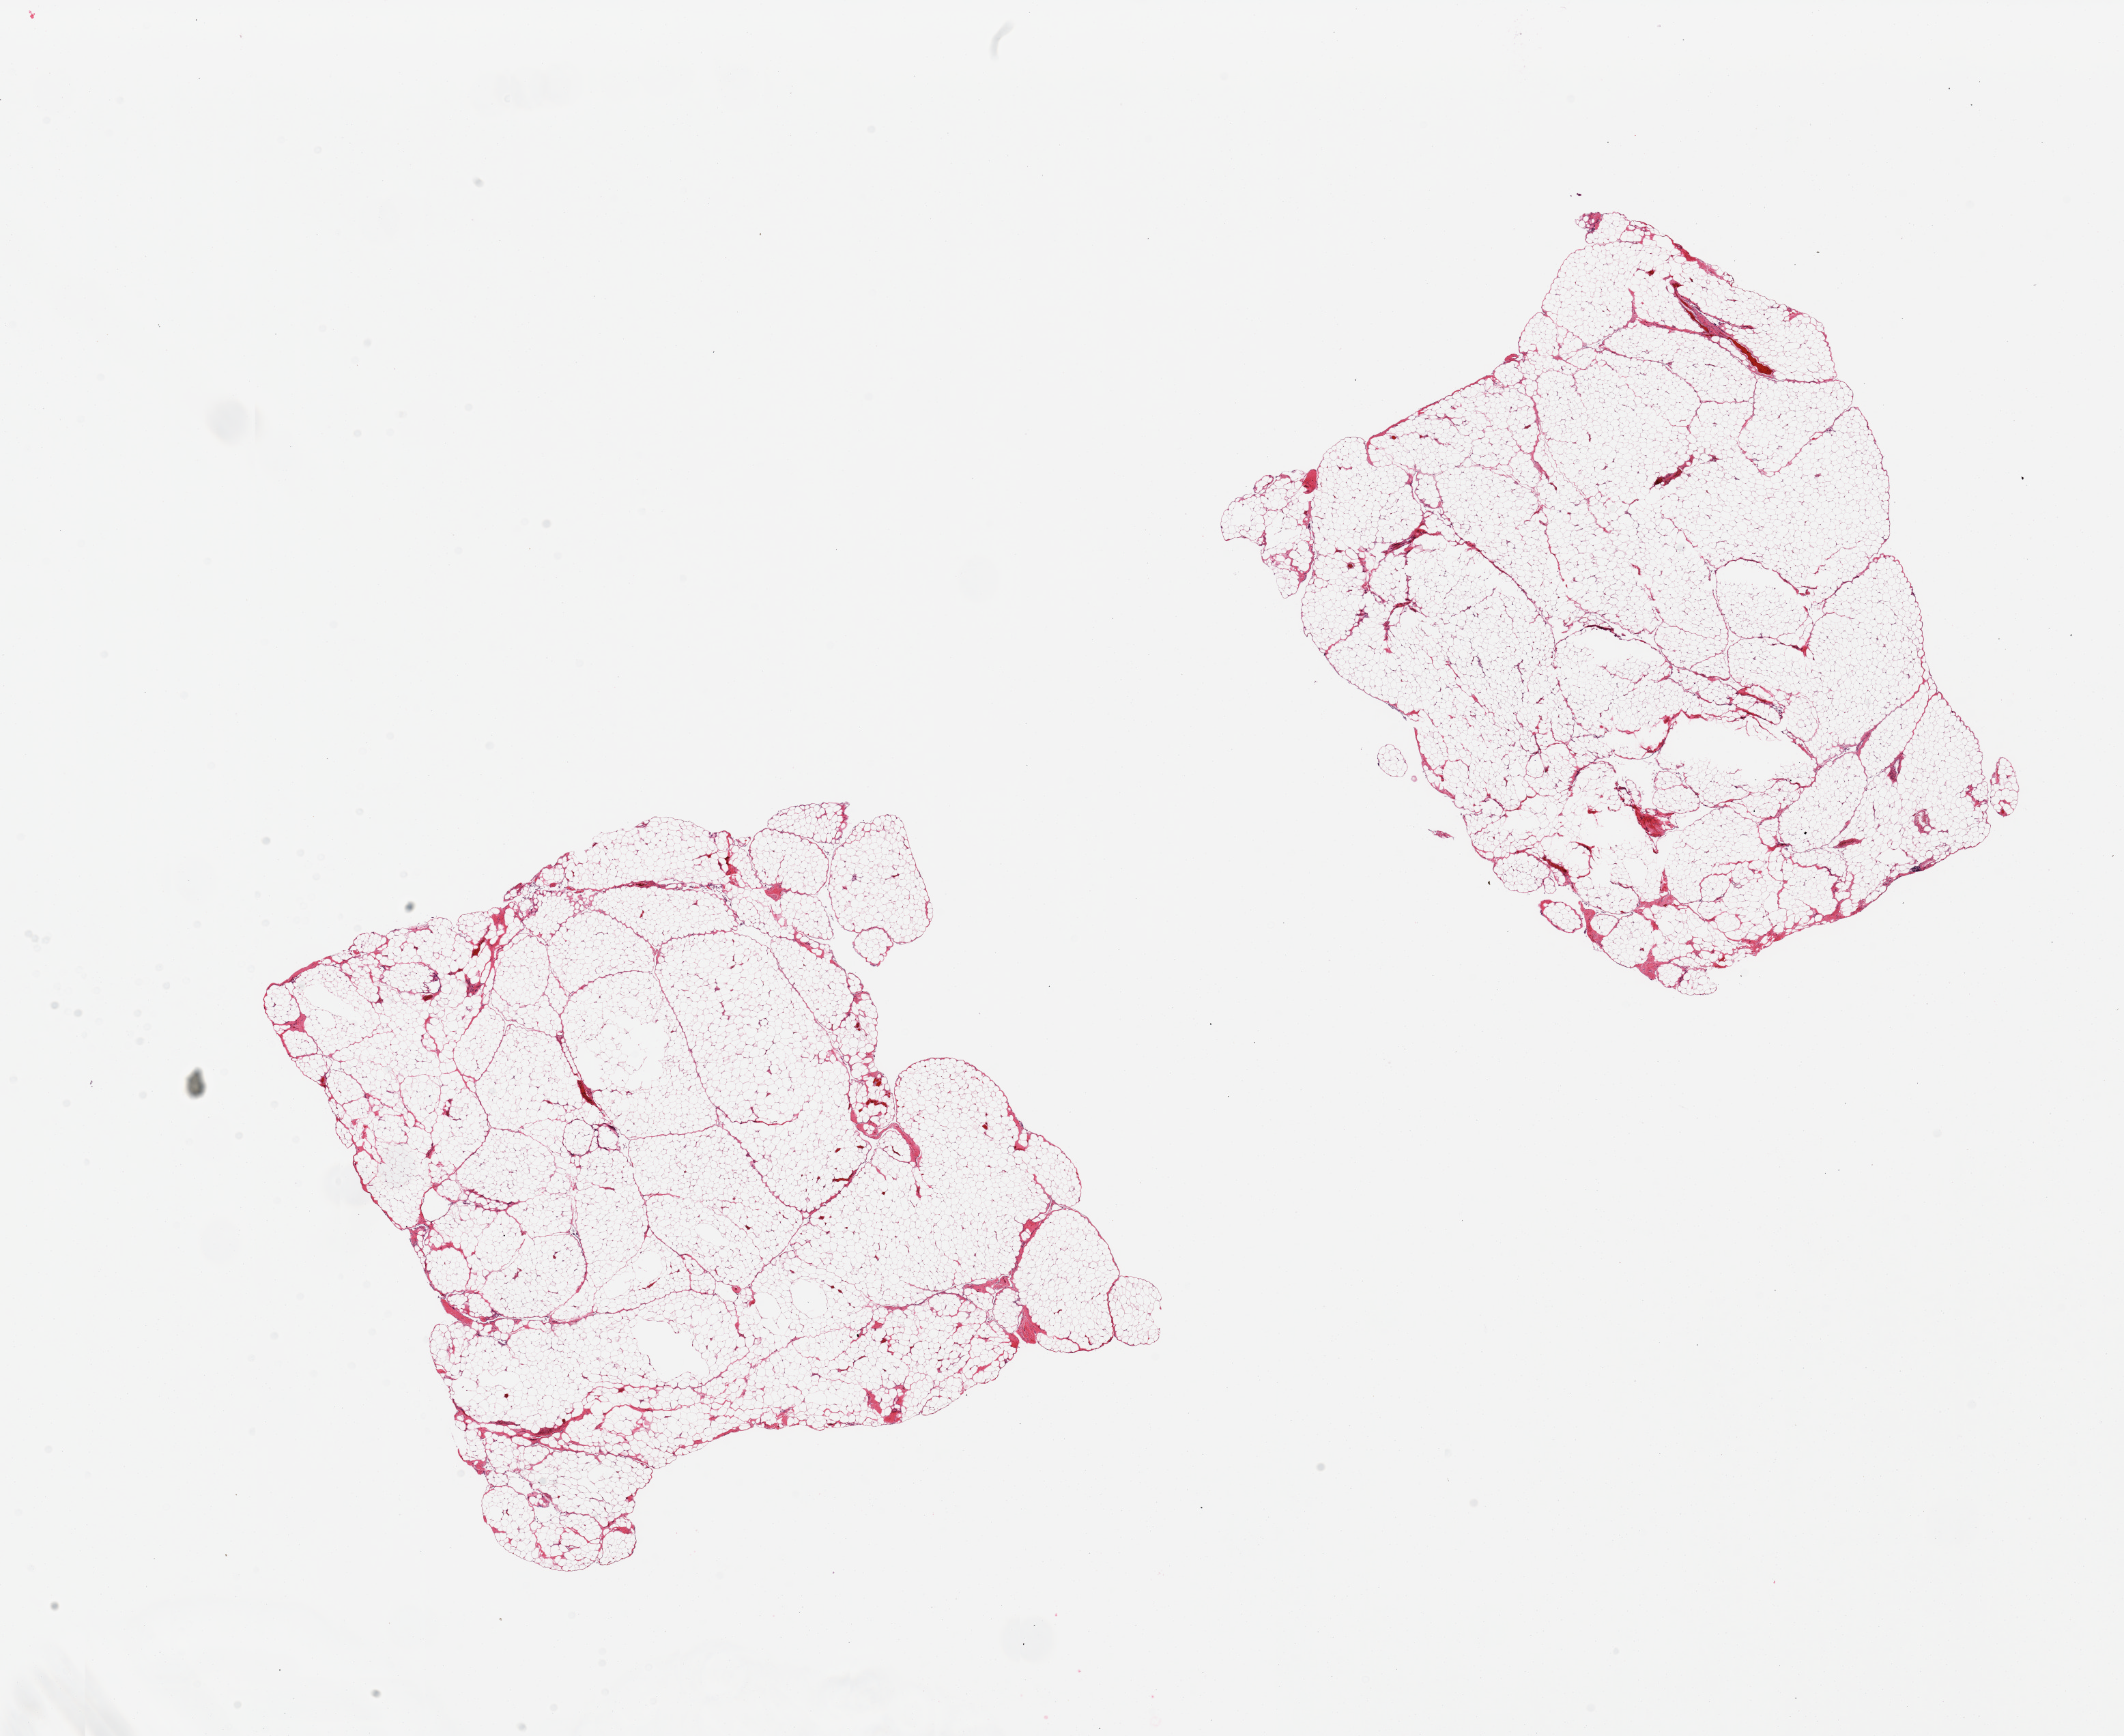
H&E whole-slide image, brightfield — a low-resolution overview of the entire scanned area, about 24.6 x 20.1 mm (acquisition: 20x scan), PAXgene-fixed, paraffin-embedded tissue, sampled site (target tissue): omentum, donor tissue sample. Donor sex: male.
* pathologist's review note for this sample: 2 pieces